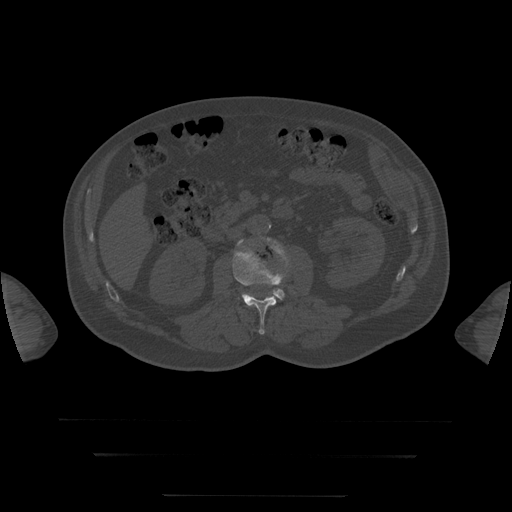
CT including the spine, one axial slice; position 16 of 397 along the scan axis; 120 kVp; bone window (W 1800 / L 400 HU); 512 × 512 image matrix, field of view 510 × 510 mm. Patient age 73 years. Case-level facts recorded for this patient, not image findings: primary cancer: prostate.
Annotated regions visible in this slice (semi-automatically segmented with operator editing):
- L3 vertebra: bounding box [x1, y1, x2, y2] px = [238, 239, 288, 300]